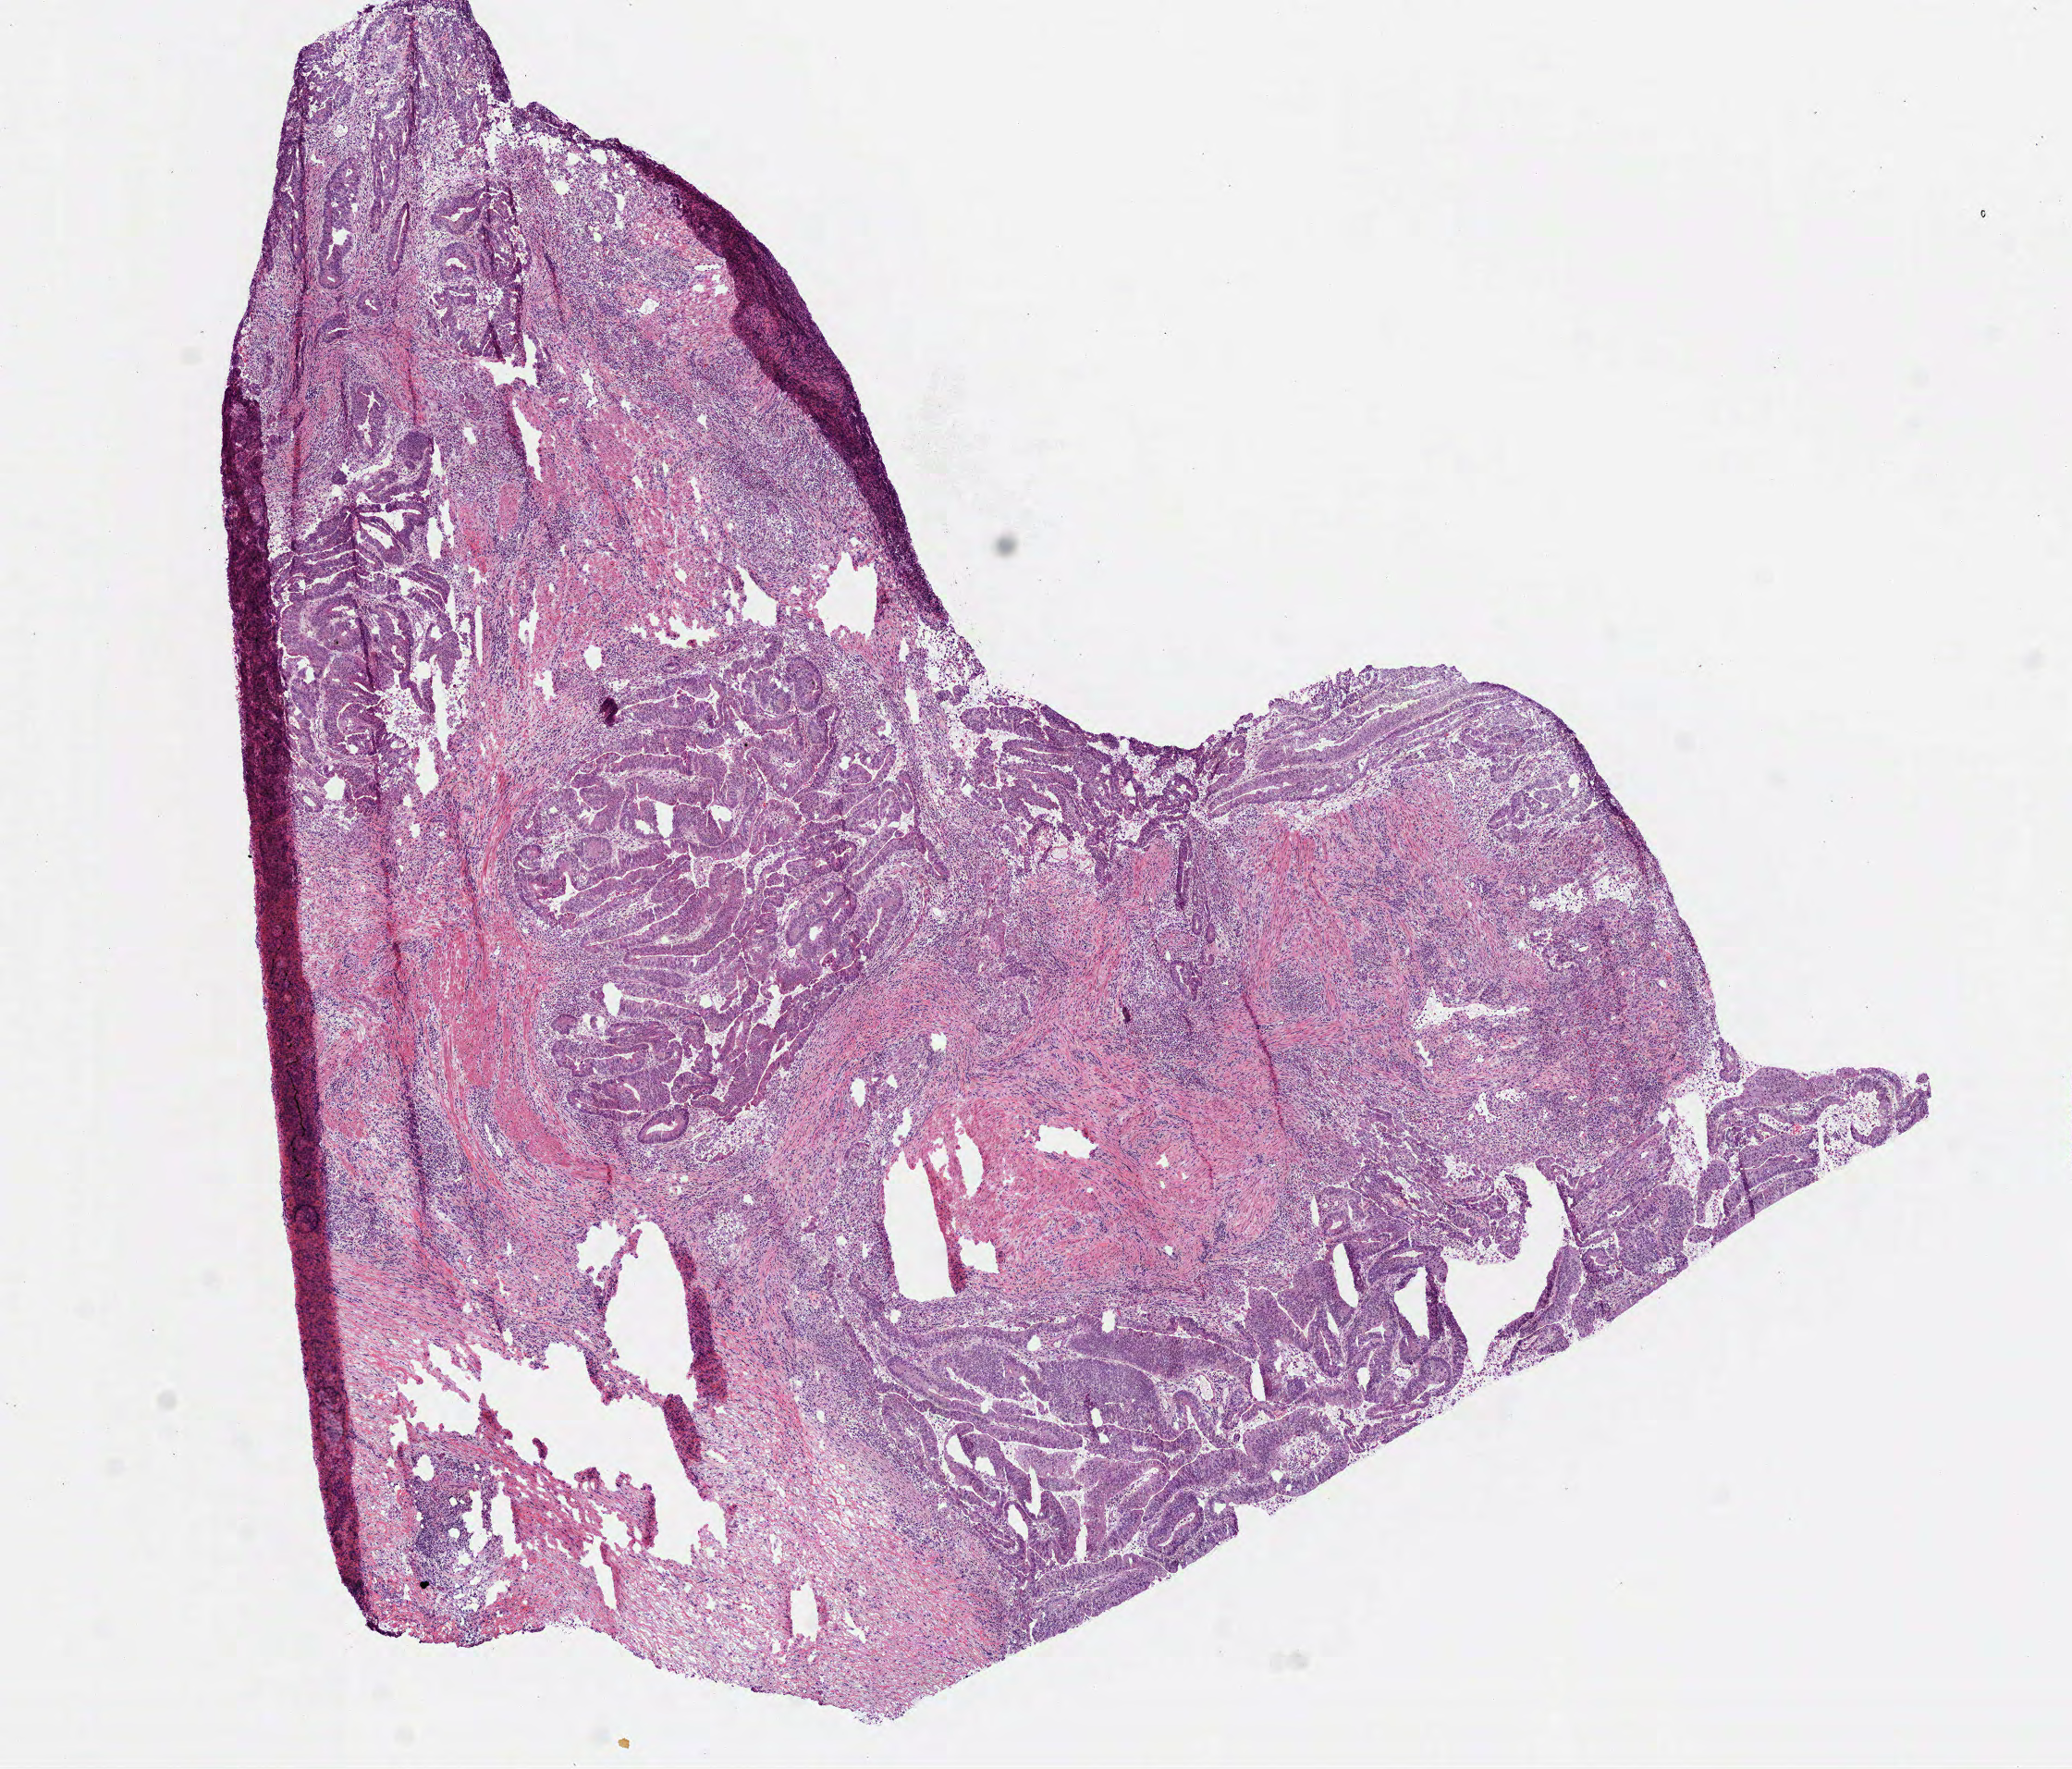
Digitized H&E tissue section (whole slide) — low-resolution overview of the scanned area, about 9.0 x 7.7 mm (slide scanned at 40x). Frozen section. Colon, primary tumour sample. Patient: male, age at initial diagnosis 61 years. Composition of this section per pathologist review: tumour cells 75%, tumour nuclei 70%, normal cells 0%, stromal cells 24%, necrosis 1%. Infiltration values recorded for this section: lymphocyte infiltration 10%, monocyte infiltration 0%, neutrophil infiltration 10%.
AJCC pathologic stage: I. TNM: T2 N0 M0. Diagnosis: Adenocarcinoma, NOS (cecum).